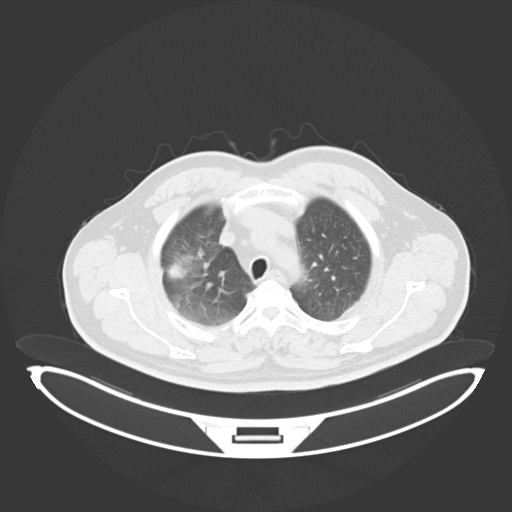
Chest CT, one axial slice. Position 228 of 284 along the scan axis. Reconstruction kernel B30f. 120 kVp. Lung window (W 1500 / L -600 HU). 512 × 512 image matrix. Patient: male, 55 years. From the clinical record (not read from this slice): clinical TNM (as recorded): T3 N2 M1.
Outlined on this slice (bounding box drawn by a radiologist):
- lung tumour (recorded histology: adenocarcinoma): bounding box (x1, y1, x2, y2) in pixels: (166, 253, 194, 282)